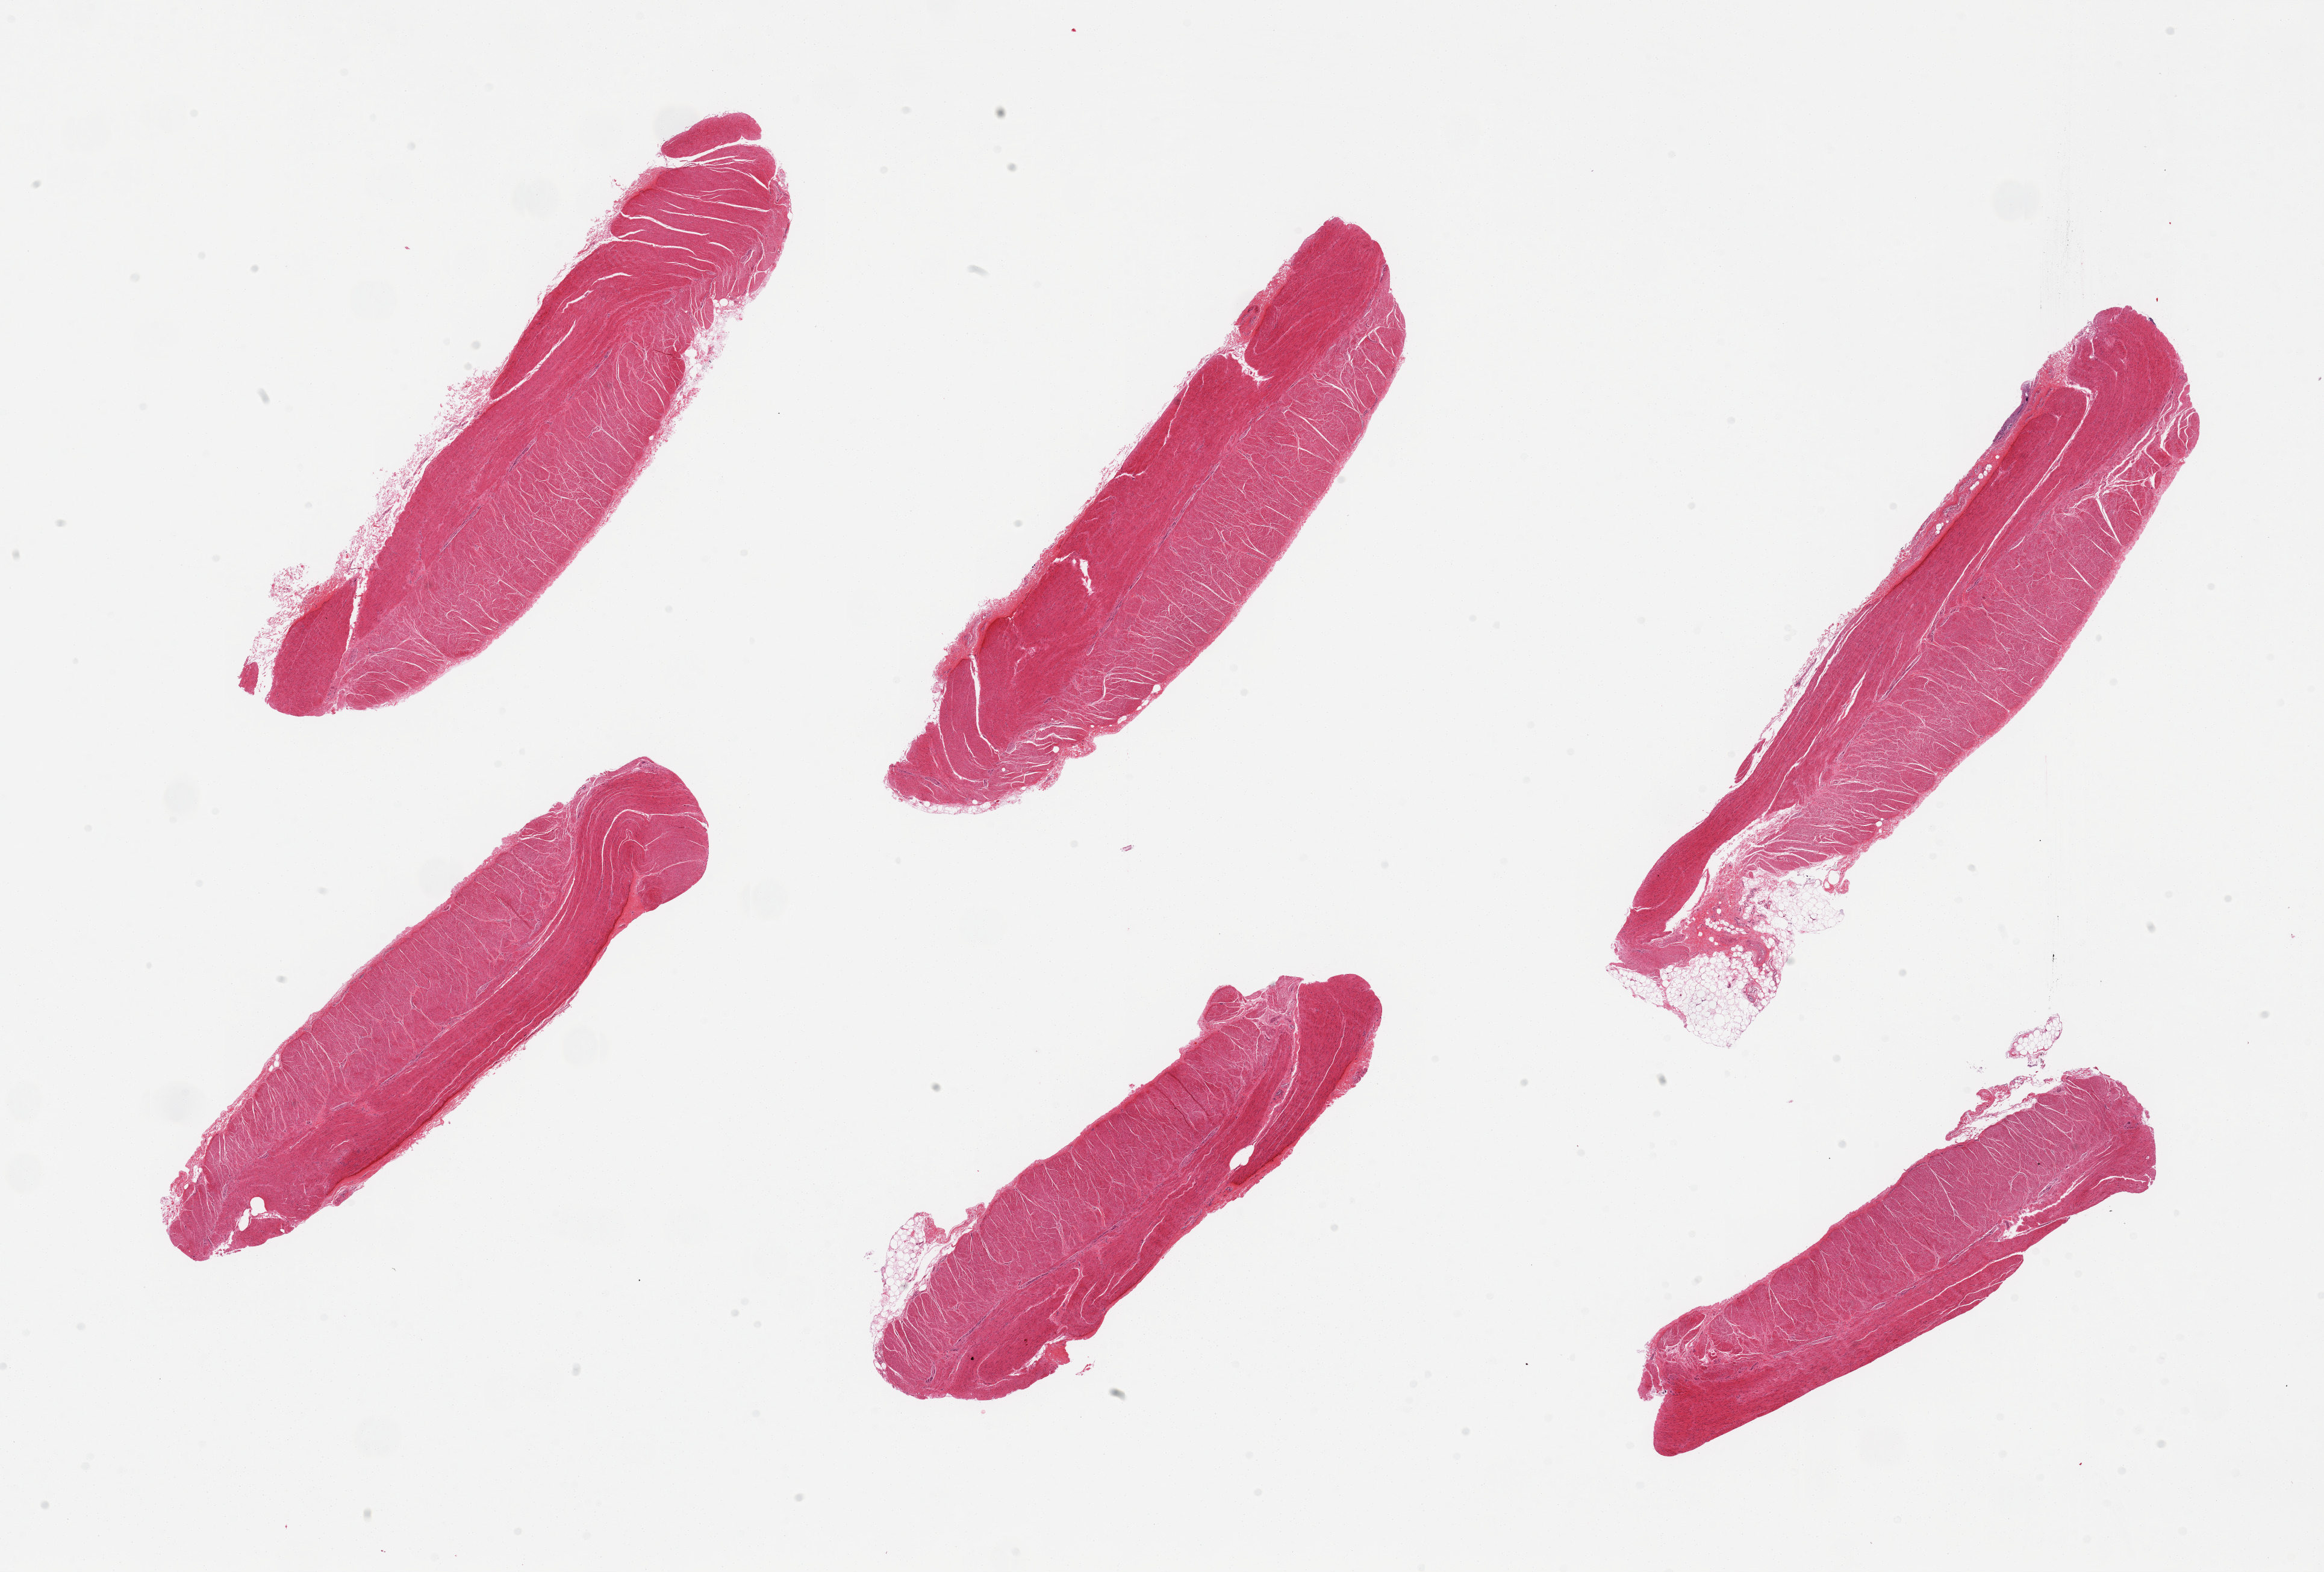
Whole-slide image, H&E stain, brightfield, low-resolution overview of the scanned area, about 30.5 x 20.6 mm (slide scanned at 20x), PAXgene-fixed paraffin-embedded (PFPE) section, section of sigmoid colon (target tissue), donor tissue sample. Donor: male.
* review note (as recorded): 6 pieces, all muscularis, good specimens